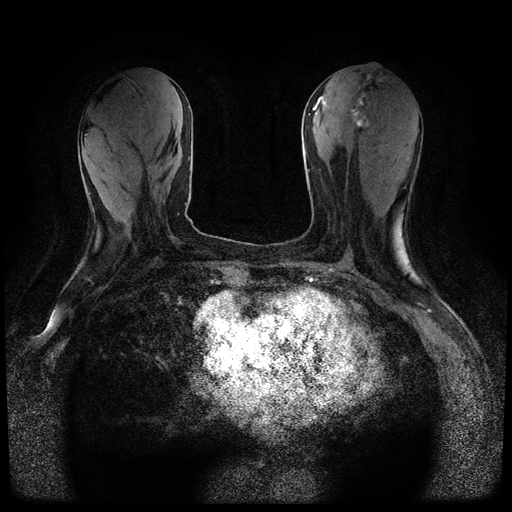
Breast MRI (dynamic contrast-enhanced, multi-phase), one axial slice. Position 28 of 116 along the scan axis. Dynamic contrast-enhanced series, time point 2 of 5 at this slice position (early post-contrast). 1.5 T. TE 2.7 ms, TR 5.4 ms. 2 mm slice thickness. 512 × 512 image matrix, field of view 320 × 320 mm. Female patient, age 80 years.
Structures marked on this image (semi-automatic segmentation, software-assisted and operator-edited):
- breast lesion (labelled 'tumour' in the annotation; benign lesions carry a separate 'benign' label): bounding box [x1, y1, x2, y2] px = [352, 75, 371, 128]